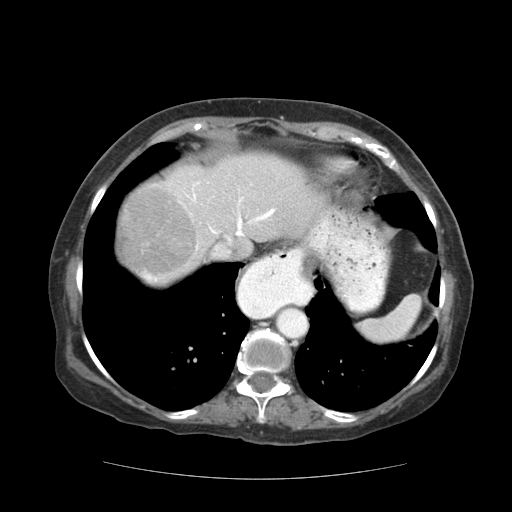
Contrast-enhanced abdominal CT (liver protocol), one axial slice; slice 94 of 111 in the series (ordered by position); reconstruction kernel STANDARD; soft-tissue window (W 400 / L 40 HU); 2.5 mm slice thickness; 512 × 512 image matrix, field of view 360 × 360 mm. From the clinical record (not read from this slice): diagnosis: hepatocellular carcinoma (patient treated with transarterial chemoembolisation; whether this scan precedes or follows treatment is not stated here); TNM stage (as recorded): Stage-I; Child-Pugh class: A; tumour nodularity: uninodular; tumour size: 7.3 cm.
Structures marked on this image (semi-automatic segmentation, software-assisted and operator-edited):
- abdominal aorta: bounding box <277,308,306,337> (left, top, right, bottom; pixels)
- liver parenchyma outside the tumour (the mass and vessels are separate outlines, so this box may not span the whole liver): <120,154,330,286>
- mass: <123,192,195,274>
- liver vessels: <145,182,275,281>